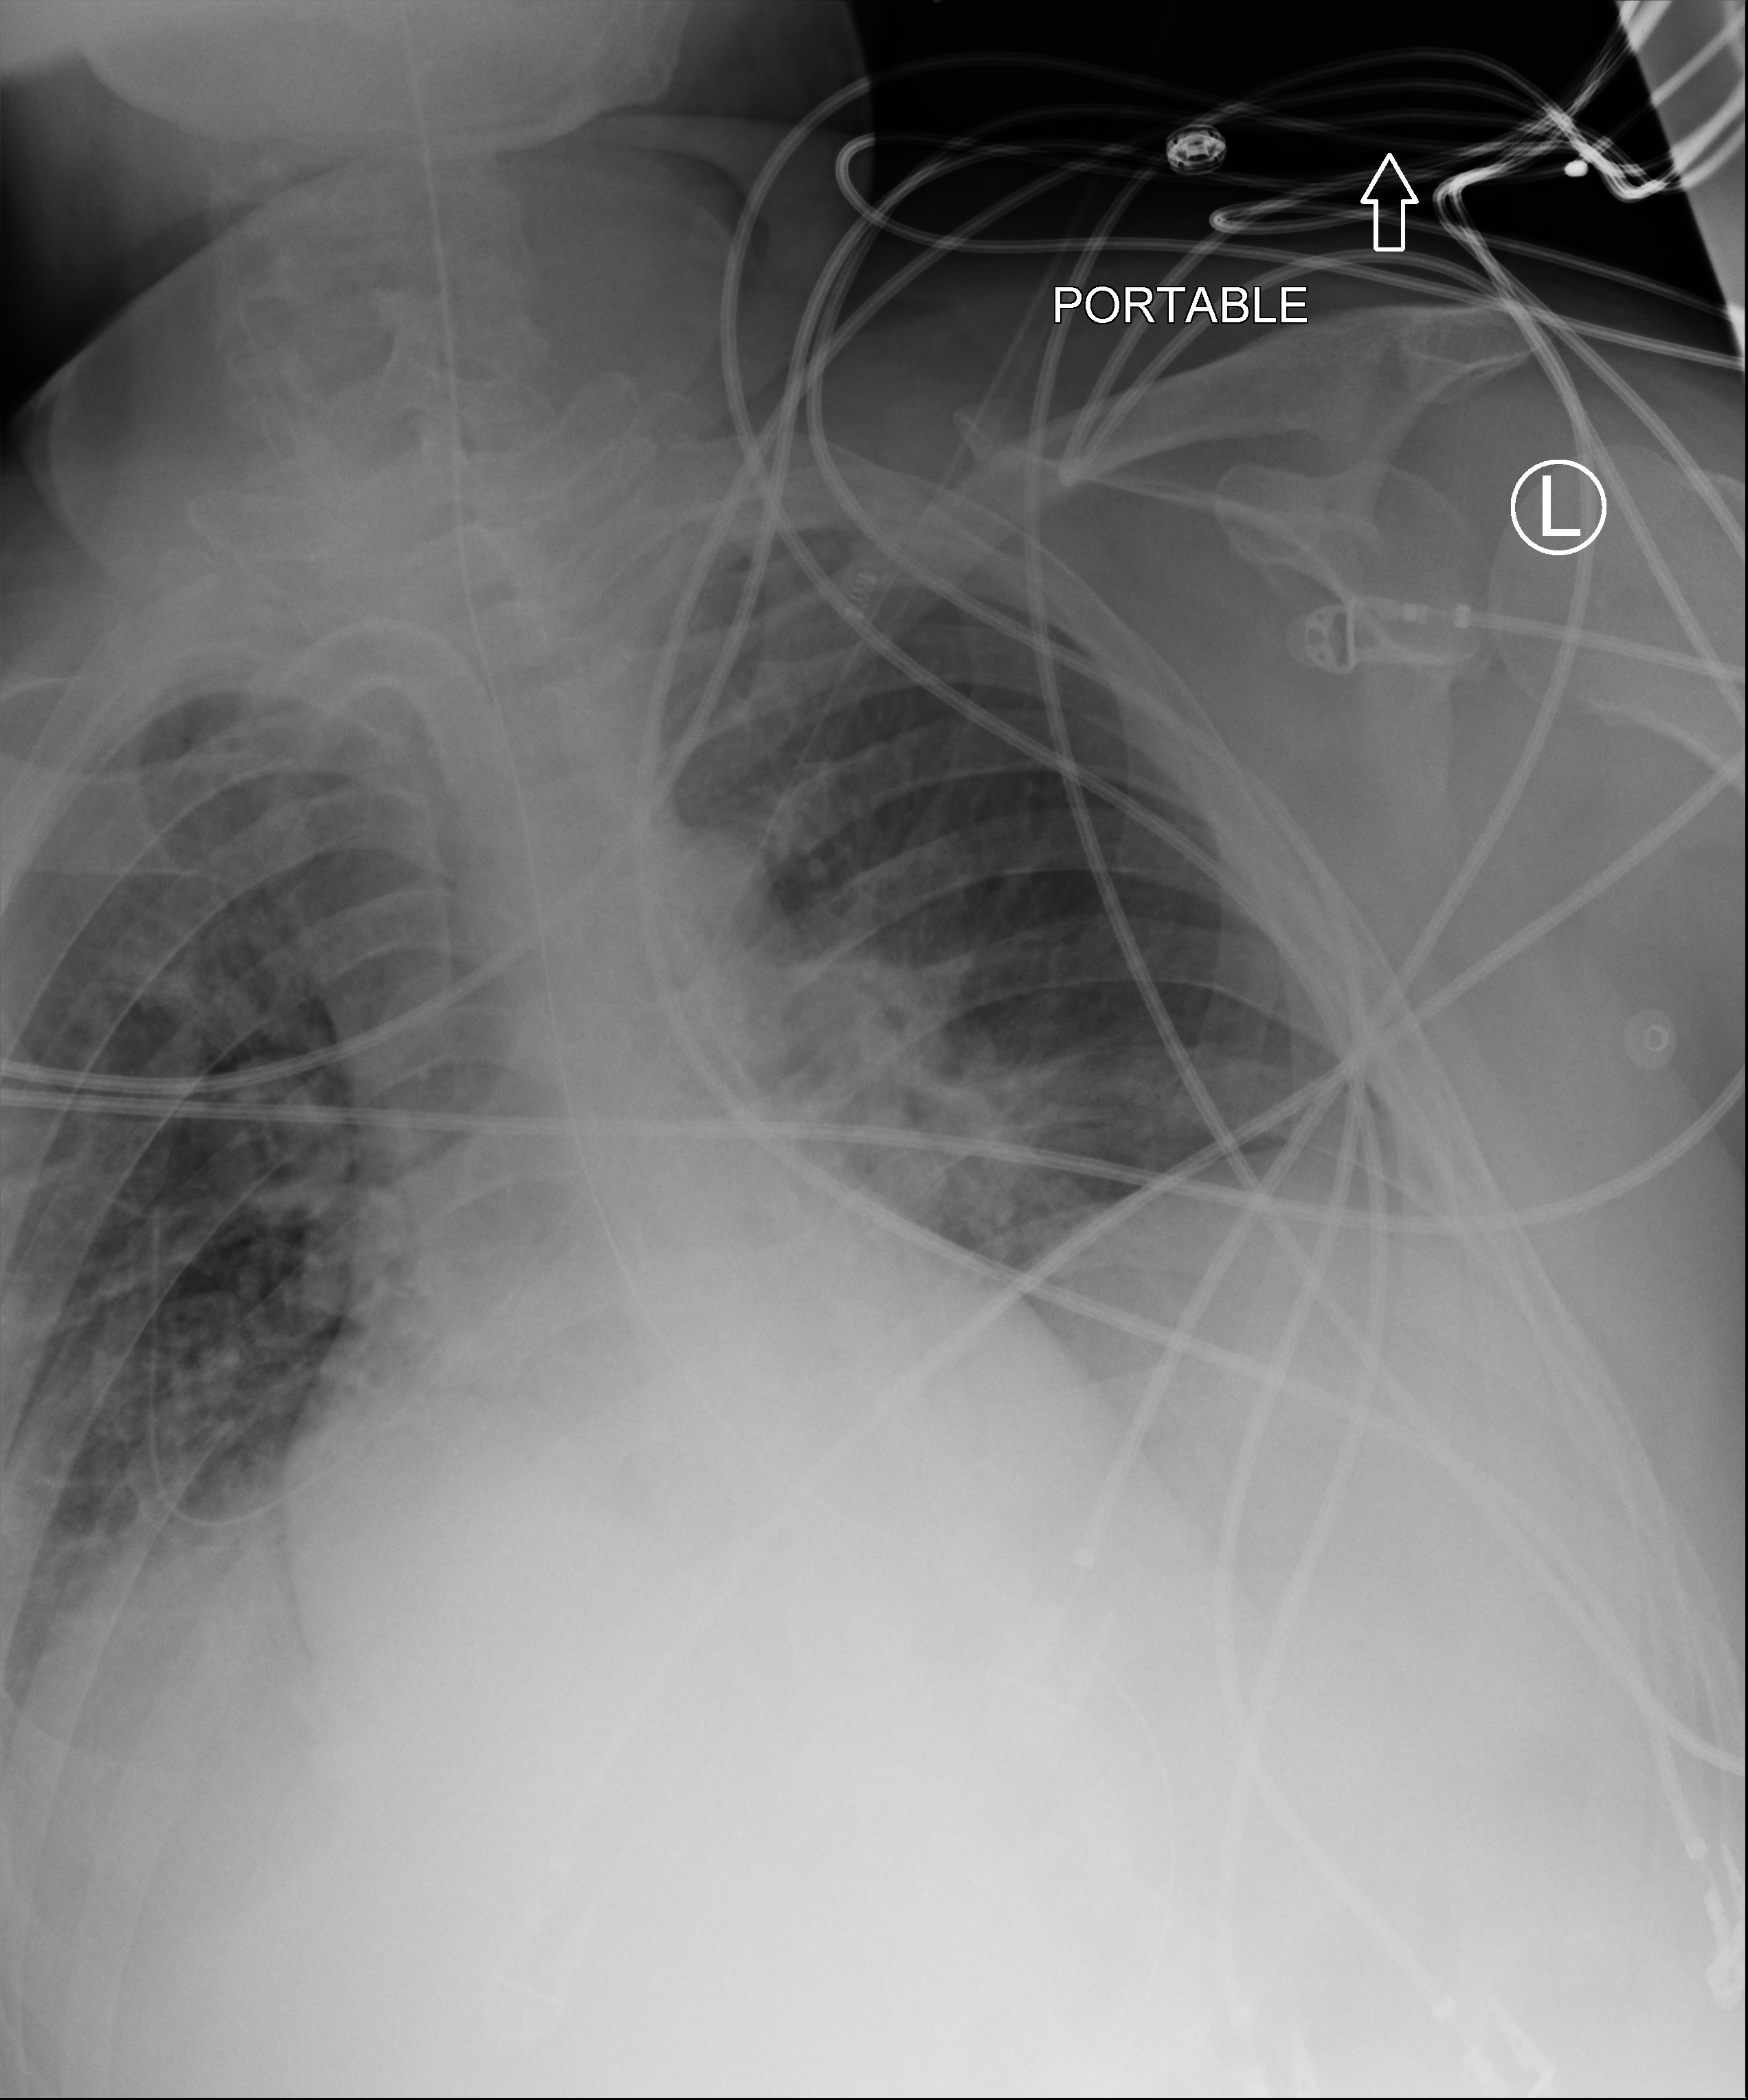
Chest X-ray (portable). Male patient hospitalised with COVID-19, age 18–59 years.
Admission-level facts for this patient (not findings on this image; timing relative to this image not recorded):
- mechanically ventilated during this hospital stay: yes